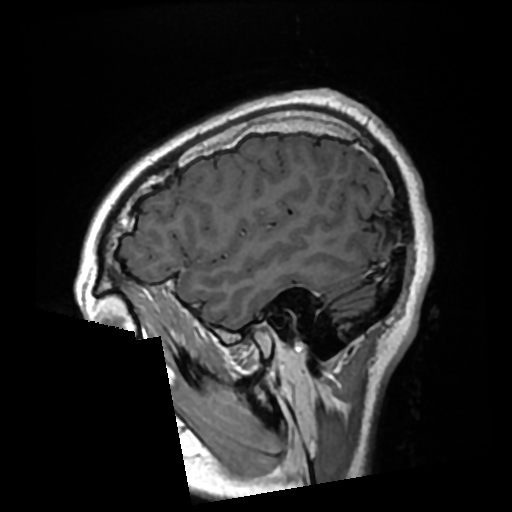
Brain MRI from a brain-tumour surgery series, one sagittal slice. Slice 71 of 276 in the series (ordered by position). T1-weighted post-contrast. 0.7 mm slice thickness. 512 × 512 image matrix. Case-level facts recorded for this patient, not image findings: histopathology: Glioma with ependymal features; WHO grade: 2; tumour location: Left Parietal.
Structures marked on this image (expert manual segmentation):
- previous resection cavity: bounding box <383,231,391,241> (left, top, right, bottom; pixels)